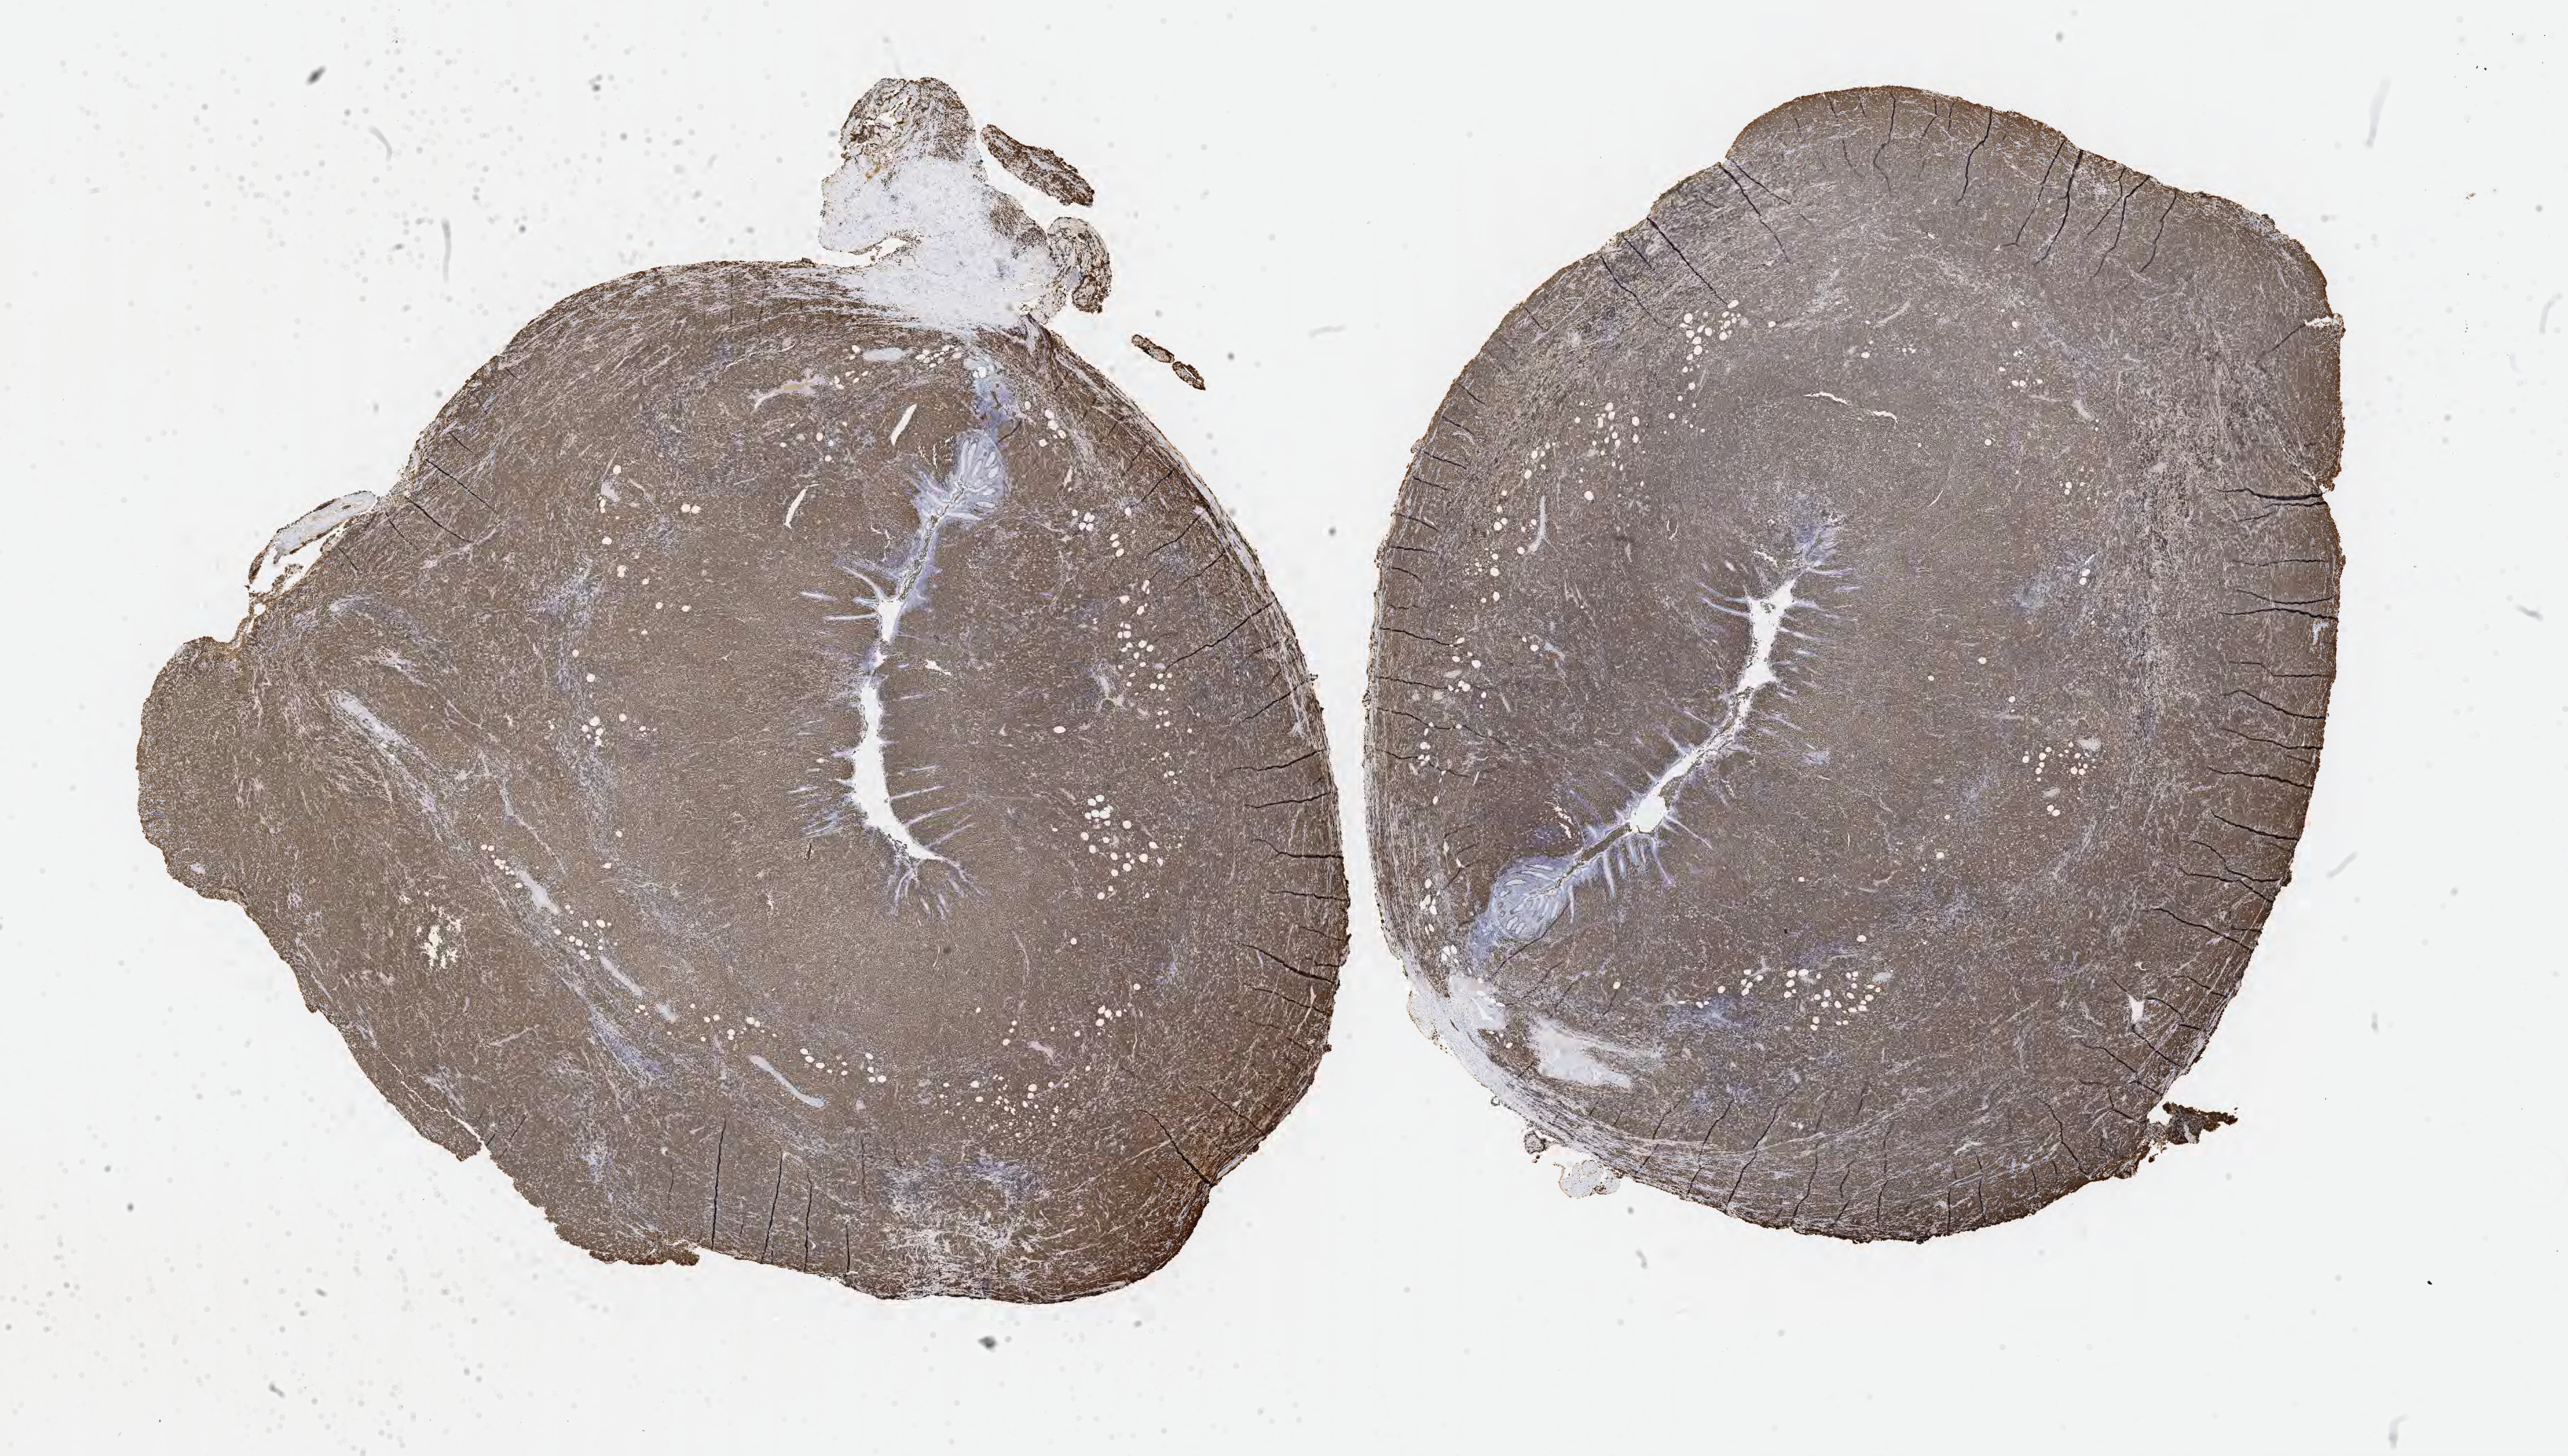
Immunohistochemistry (IHC) whole-slide image stained for Ki-67, whole scanned area (about 30.2 x 17.1 mm) shown as a low-resolution overview; tumor tissue. Male patient, aged 63.
- diagnosis: Diffuse large B-cell lymphoma, NOS